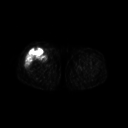
FDG PET of an extremity soft-tissue mass (from a PET/CT study), one axial slice; slice 233 of 311 in the series (ordered by position); 3.27 mm slice thickness; 128 × 128 image matrix. Female patient, age 57 years. Case-level facts recorded for this patient, not image findings: histological type: pleiomorphic undifferentiated sarcoma; grade: high; site of the primary tumour: right quadricep.
Structures marked on this image (expert contour drawn on MRI and transferred to this co-registered scan by the dataset authors):
- tumour plus oedema (research contour): bounding box <25,49,46,71> (left, top, right, bottom; pixels)
- tumour (research contour): <25,49,46,71>